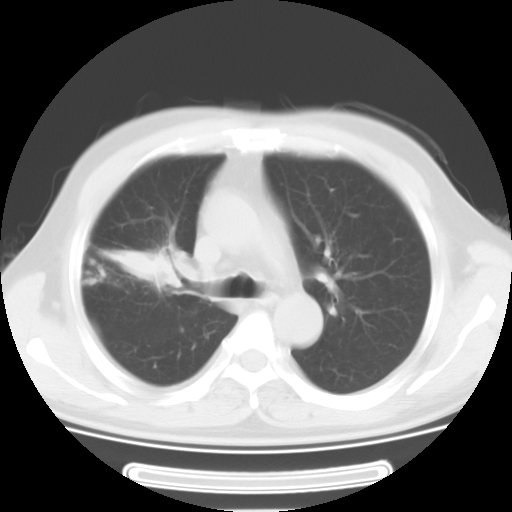
Chest CT, one axial slice. Slice 20 of 29 in the series (ordered by position). 120 kVp. Lung window (W 1500 / L -600 HU). 10 mm slice thickness. 512 × 512 image matrix, field of view 350 × 350 mm. Male patient, age 46 years. From the clinical record (not read from this slice): clinical TNM (as recorded): T3 N0 M1b.
Annotated regions visible in this slice (rectangle marked by the reading radiologist):
- lung tumour (recorded histology: adenocarcinoma): bounding box (x1, y1, x2, y2) in pixels: (92, 236, 189, 300)